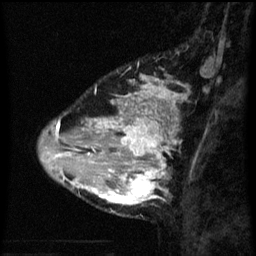
Breast MRI (dynamic contrast-enhanced), one sagittal slice. Slice 18 of 60 in the series (ordered by position). Dynamic contrast-enhanced series, image 2 of 3 at this slice position (ordered by acquisition). 1.5 T. TE 4.2 ms, TR 8 ms. 2.3 mm slice thickness. 256 × 256 image matrix, field of view 180 × 180 mm. Patient: female, 33 years.
Annotated regions visible in this slice (semi-automatically segmented with operator editing):
- analysis volume of interest (the breast-tissue region the enhancement analysis was run in; not a lesion): bounding box <71,118,171,207> (left, top, right, bottom; pixels)
- tumour enhancement mask (voxels above the 70 % enhancement threshold inside the analysis volume of interest): <72,118,169,205>